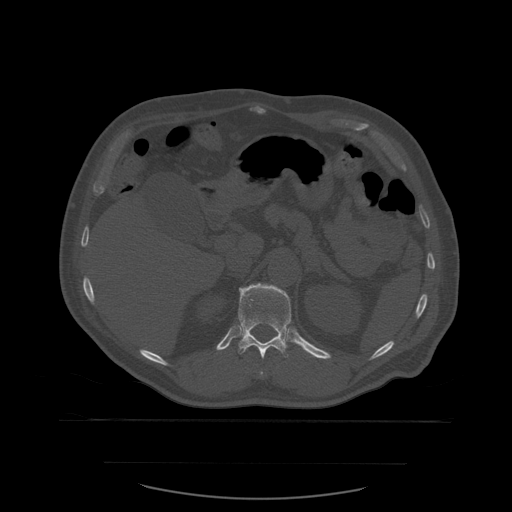
CT including the spine, one axial slice. Position 272 of 590 along the scan axis. Bone window (W 1800 / L 400 HU). 1.25 mm slice thickness. 512 × 512 image matrix, field of view 479 × 479 mm. Patient age 71 years. From the clinical record (not read from this slice): primary cancer: lung; vertebrae with lytic lesions (as recorded): T1, T2, L5, S1.
Outlined on this slice (semi-automatic segmentation, software-assisted and operator-edited):
- T12 vertebra: bounding box (x1, y1, x2, y2) in pixels: (238, 283, 292, 375)